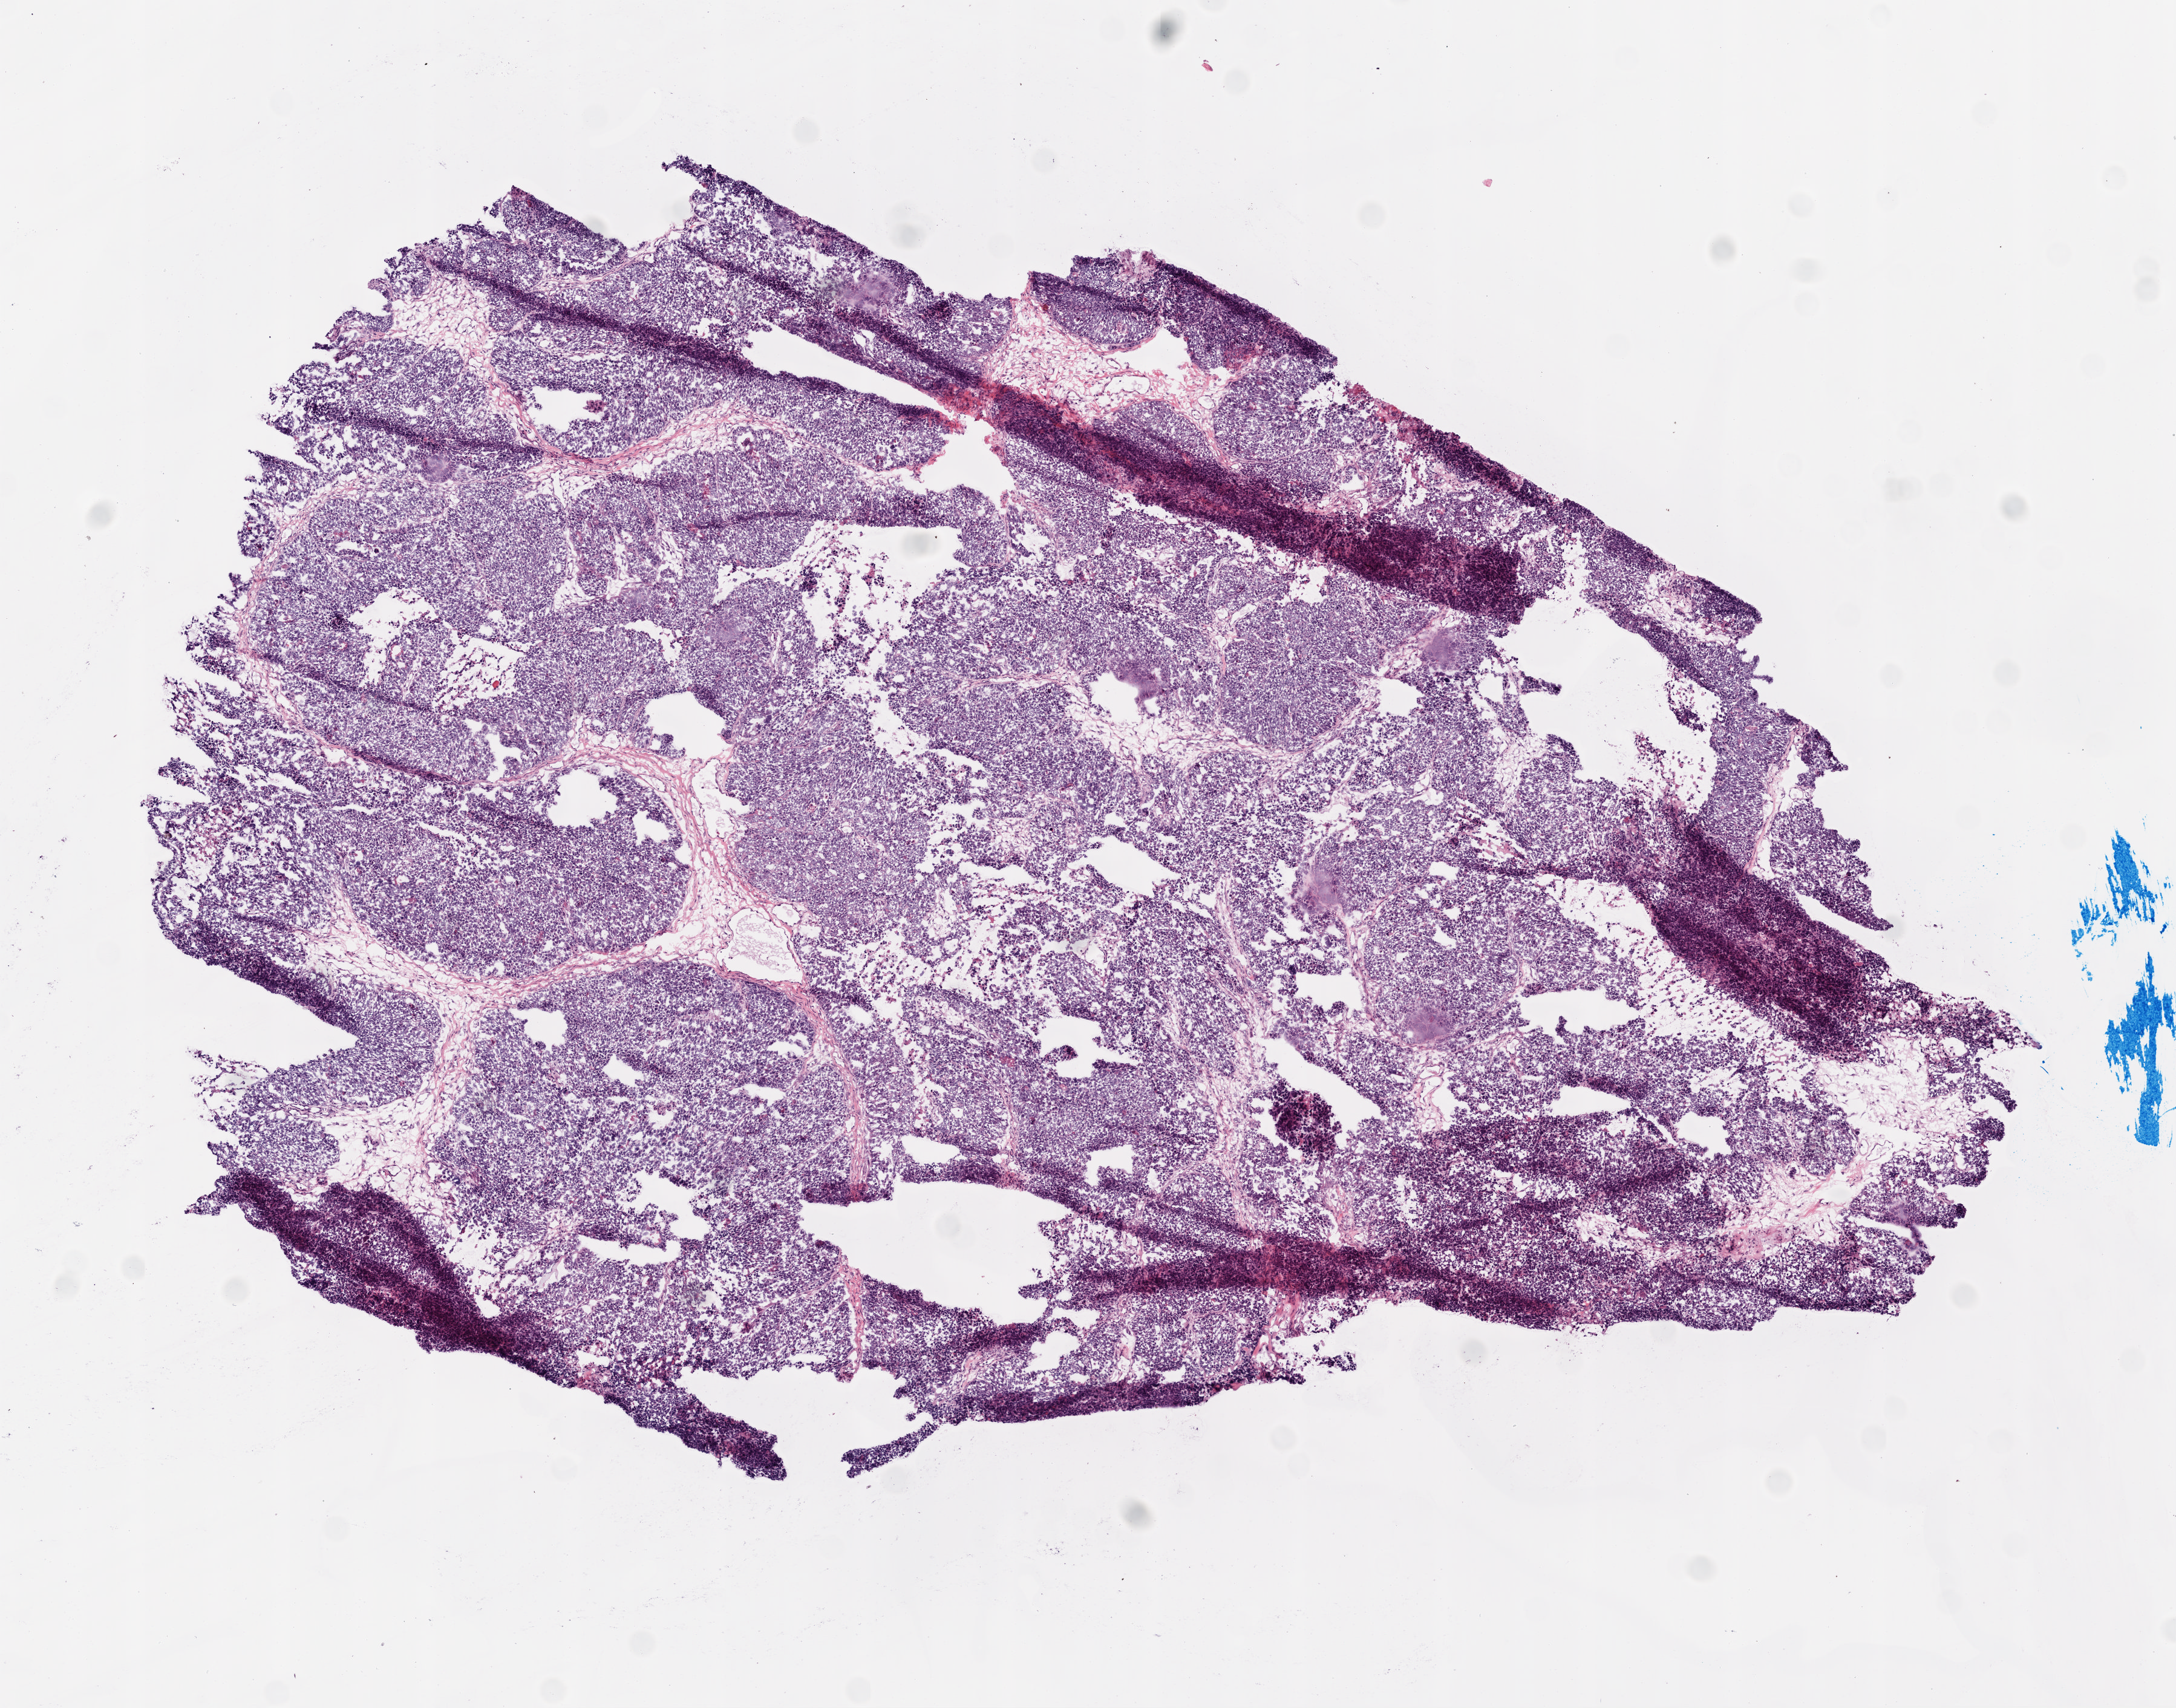
Digitized H&E tissue section (whole slide) — a low-resolution overview of the entire scanned area, about 7.3 x 5.7 mm, frozen section, ovary, primary tumour sample. Patient: female, age at initial diagnosis 42 years. Histologic grade: G3 (poorly differentiated). Slide review estimates, as recorded: tumour nuclei 95%, normal cells 0%, necrosis 0%.
* laterality: right
* FIGO stage: IIIC
* pathologic diagnosis: Serous cystadenocarcinoma, NOS